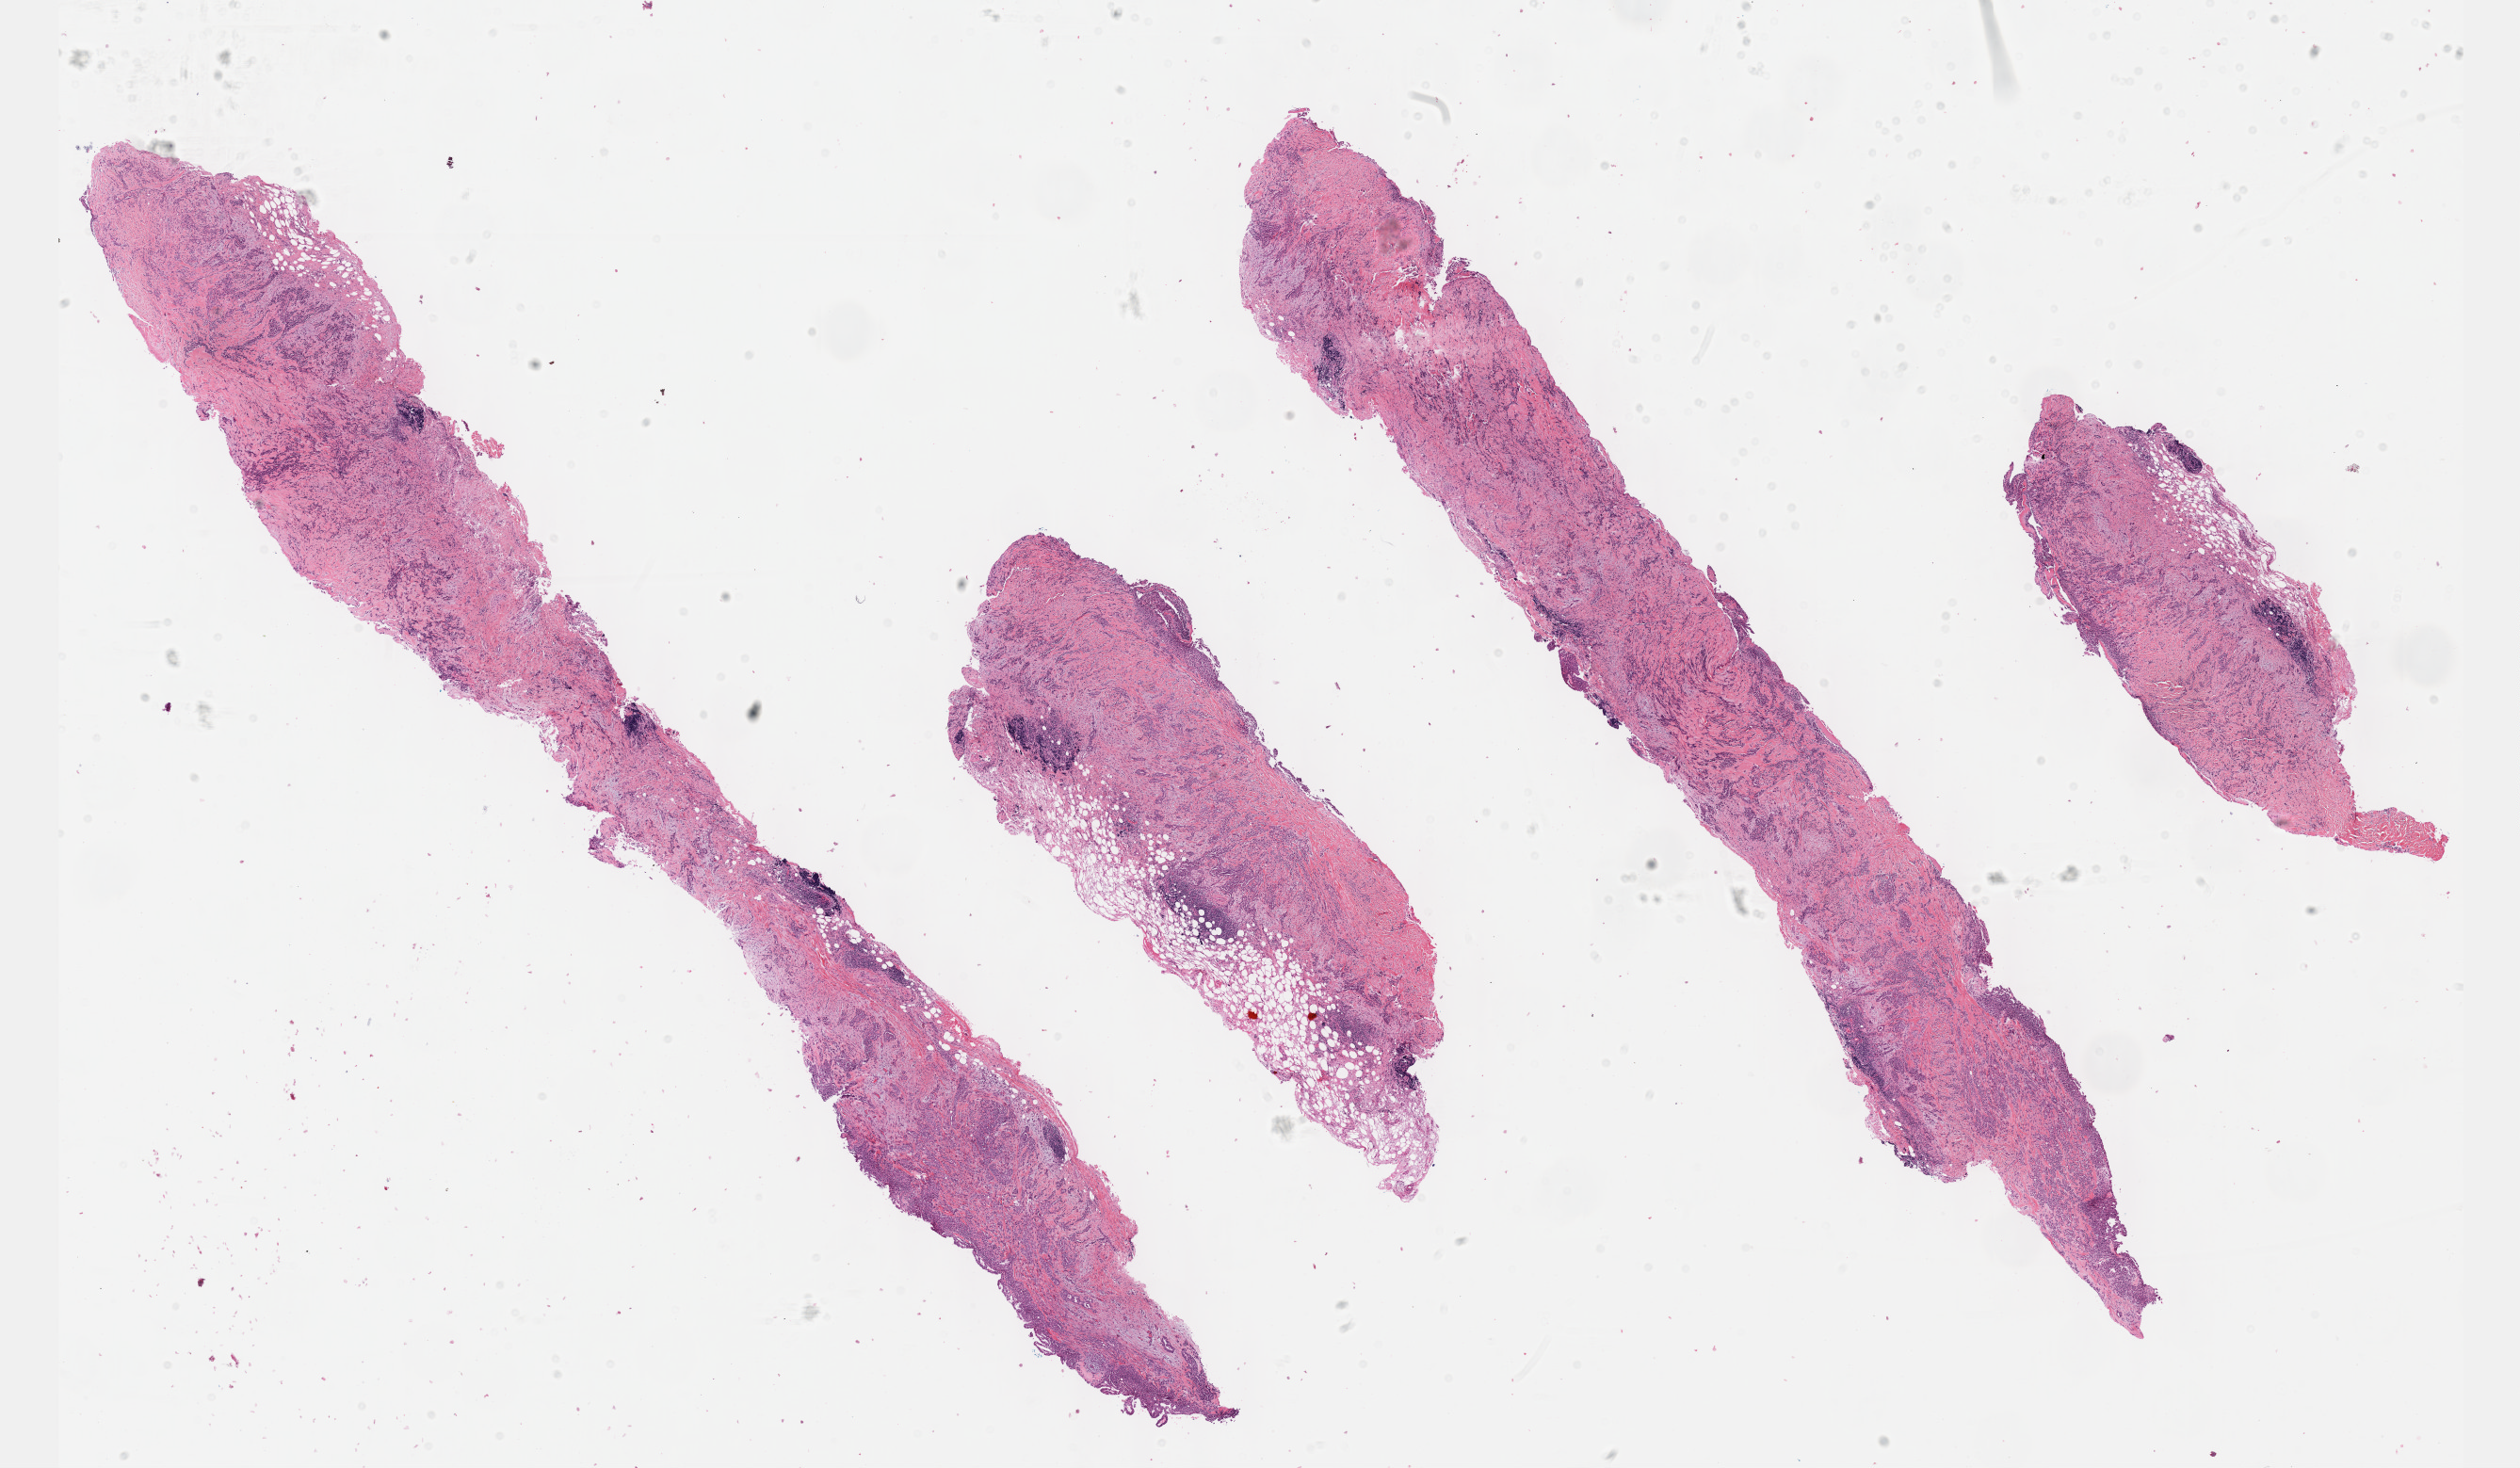
Hematoxylin and eosin (H&E) stained whole-slide image — low-resolution overview of the scanned area, about 21.6 x 12.6 mm (from a 40x scan). Formalin-fixed paraffin-embedded (FFPE) diagnostic section. Primary tumour sample from the mesothelium. Male, age 66 years at initial diagnosis.
- pathologic diagnosis: Epithelioid mesothelioma, malignant (pleura, NOS)
- AJCC pathologic stage: II (7th edition)